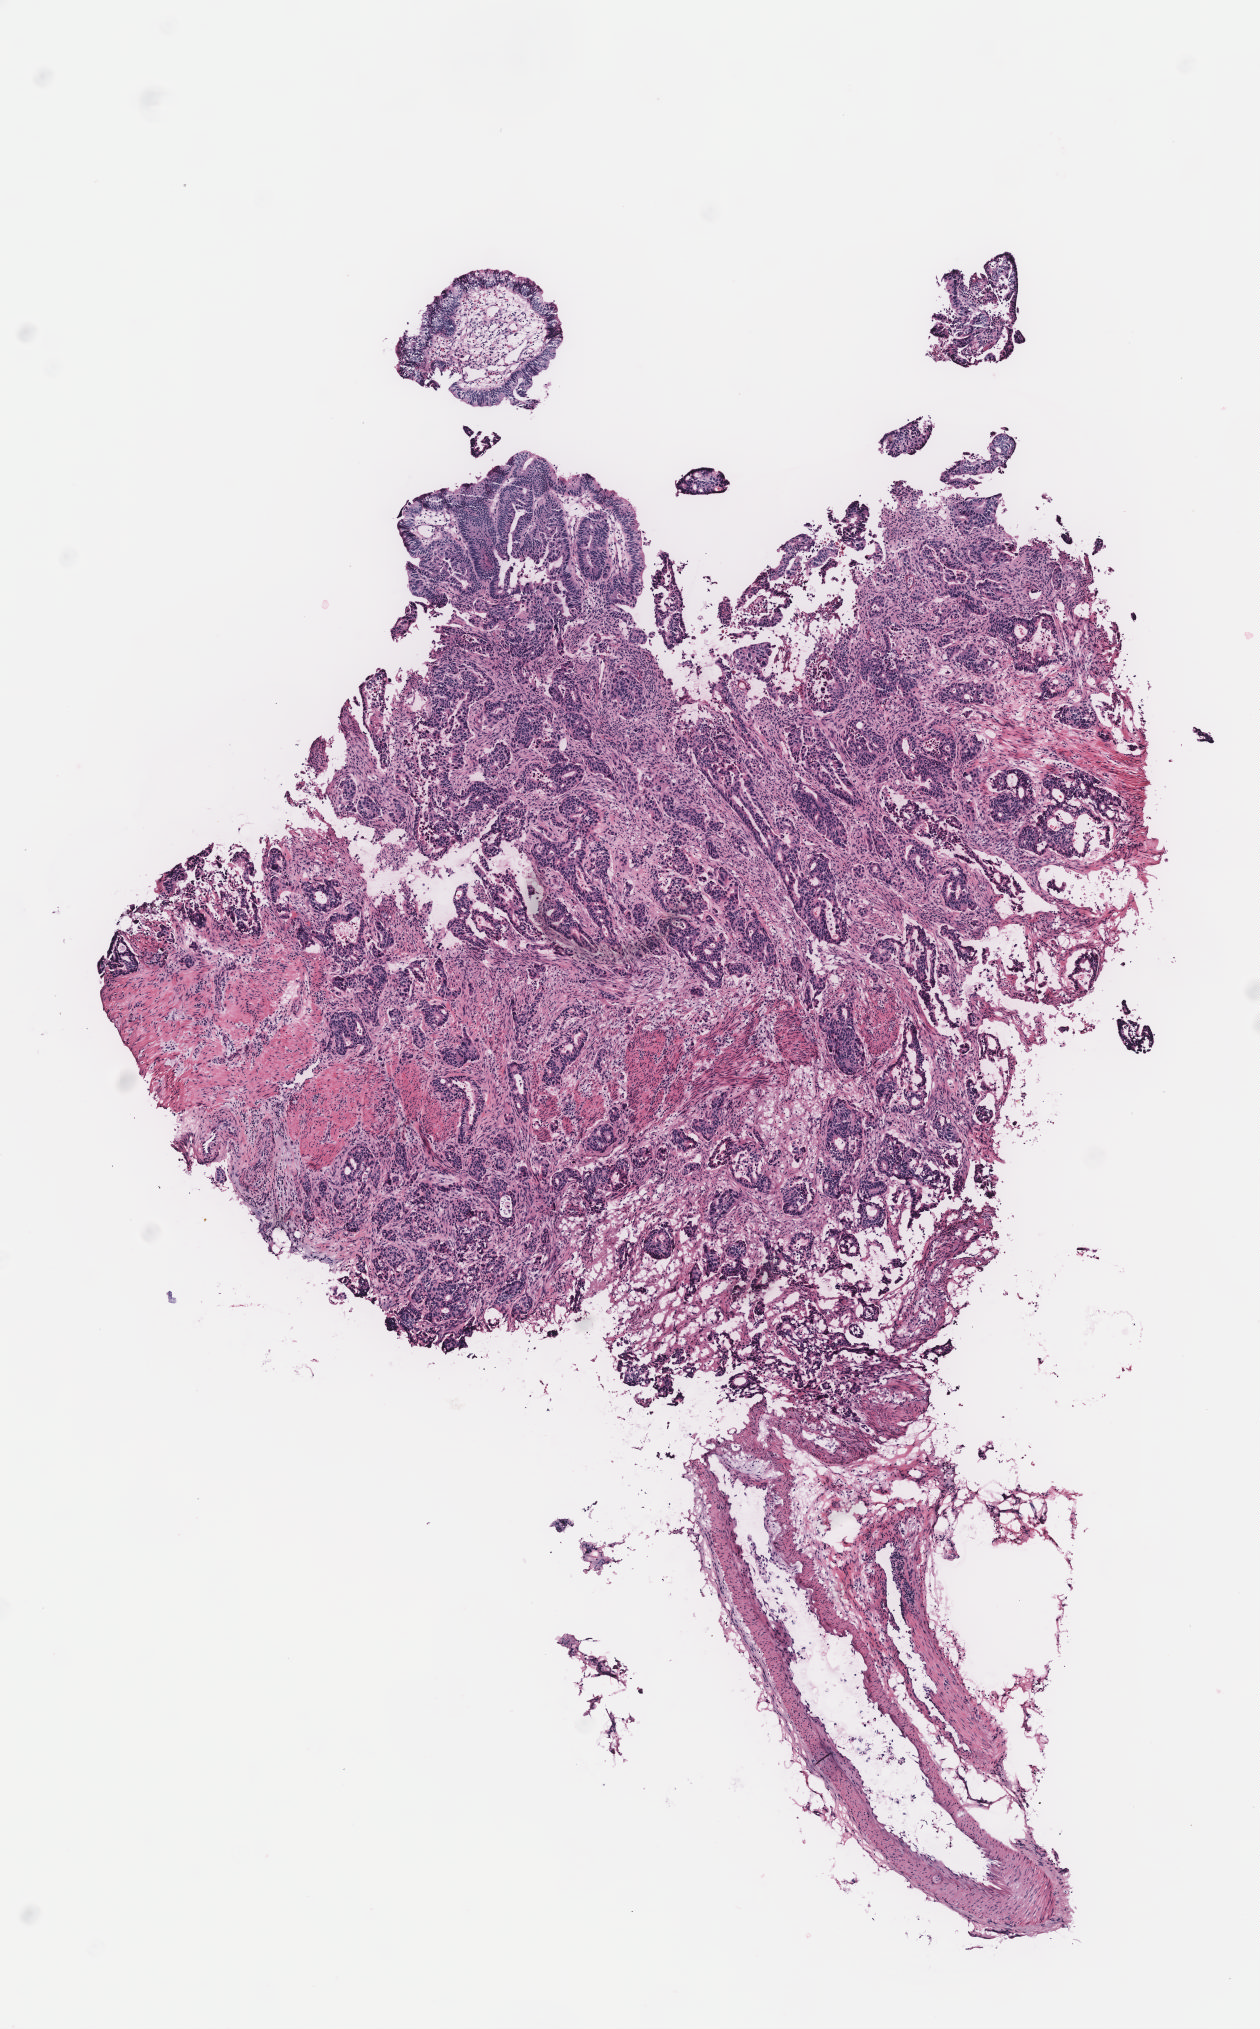
Digitized H&E-stained tissue section (whole slide), a low-resolution overview of the entire scanned area, about 5.0 x 8.1 mm, normal (non-tumour) tissue sample, colon. Female, 73 y/o.
This section: normal (non-tumour) tissue from the same patient. Patient diagnosis: Adenocarcinoma, NOS.